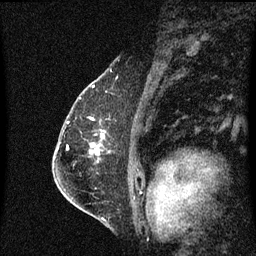
Breast MRI (dynamic contrast-enhanced), one sagittal slice. Slice 44 of 60 in the series (ordered by position). Dynamic contrast-enhanced series, image 2 of 3 at this slice position (ordered by acquisition). 1.5 T. TE 4.2 ms, TR 8.4 ms. 2 mm slice thickness. 256 × 256 image matrix. Female patient, age 57 years. Case-level facts recorded for this patient, not image findings: setting: breast cancer imaged before/during neoadjuvant chemotherapy; receptor status: HR-positive, HER2-negative.
Outlined on this slice (semi-automatic segmentation, software-assisted and operator-edited):
- analysis volume of interest (the breast-tissue region the enhancement analysis was run in; not a lesion): bounding box [x1, y1, x2, y2] px = [92, 130, 107, 145]
- tumour enhancement mask (voxels above the 70 % enhancement threshold inside the analysis volume of interest): [103, 136, 105, 139]